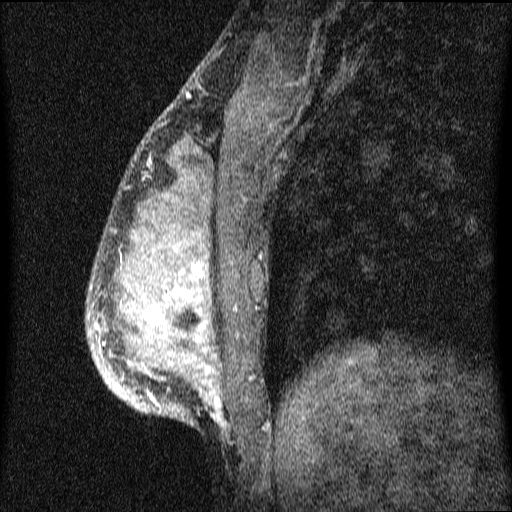
Breast MRI (dynamic contrast-enhanced), one sagittal slice. Slice 21 of 64 in the series (ordered by position). Dynamic contrast-enhanced series, image 2 of 4 at this slice position (ordered by acquisition). 1.5 T. TE 4.2 ms, TR 9.1 ms. 512 × 512 image matrix, field of view 180 × 180 mm. Patient: female, 33 years.
Annotated regions visible in this slice (semi-automatically segmented with operator editing):
- analysis volume of interest (the breast-tissue region the enhancement analysis was run in; not a lesion): bounding box [x1, y1, x2, y2] px = [87, 151, 333, 447]
- tumour enhancement mask (voxels above the 70 % enhancement threshold inside the analysis volume of interest): [97, 236, 223, 422]